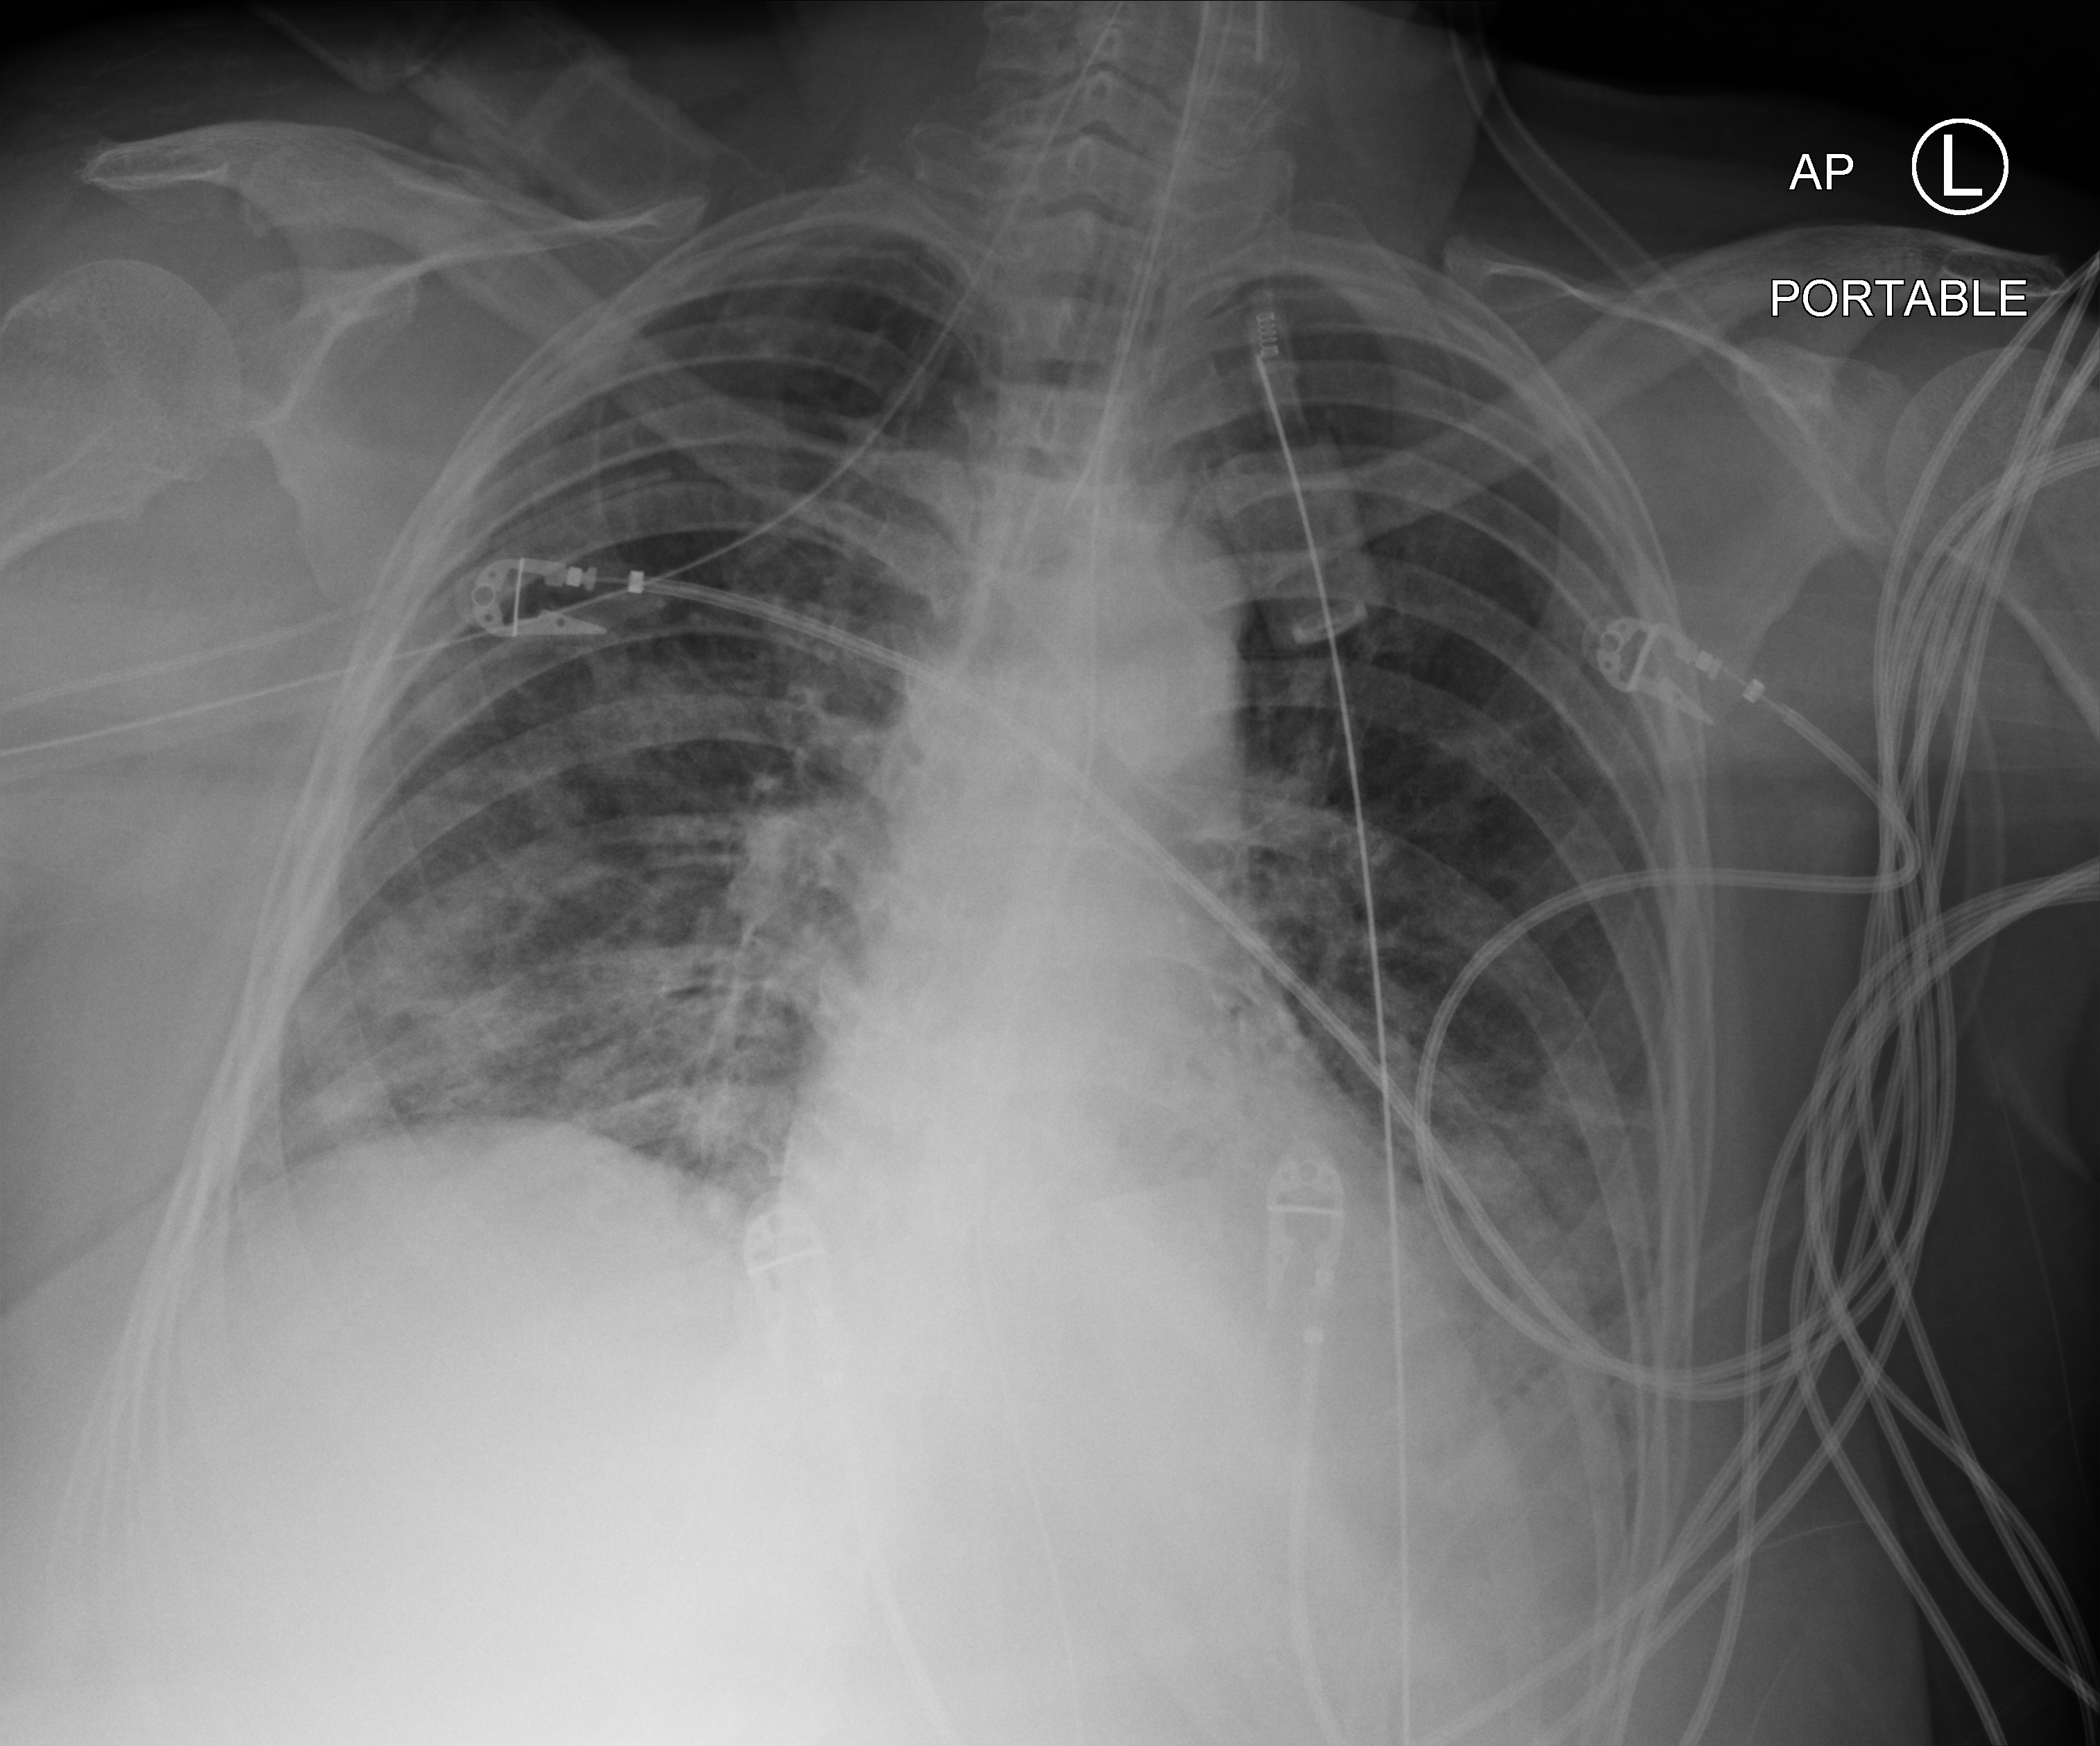
Bedside chest radiograph (computed radiography). Patient hospitalised with COVID-19; female, aged 75–90 years.
From the hospital-stay record, not from the radiograph (when in the stay this image was taken is not recorded): mechanically ventilated during this hospital stay: yes; other chronic lung disease (admission record): no; admitted to intensive care during this hospital stay: yes.